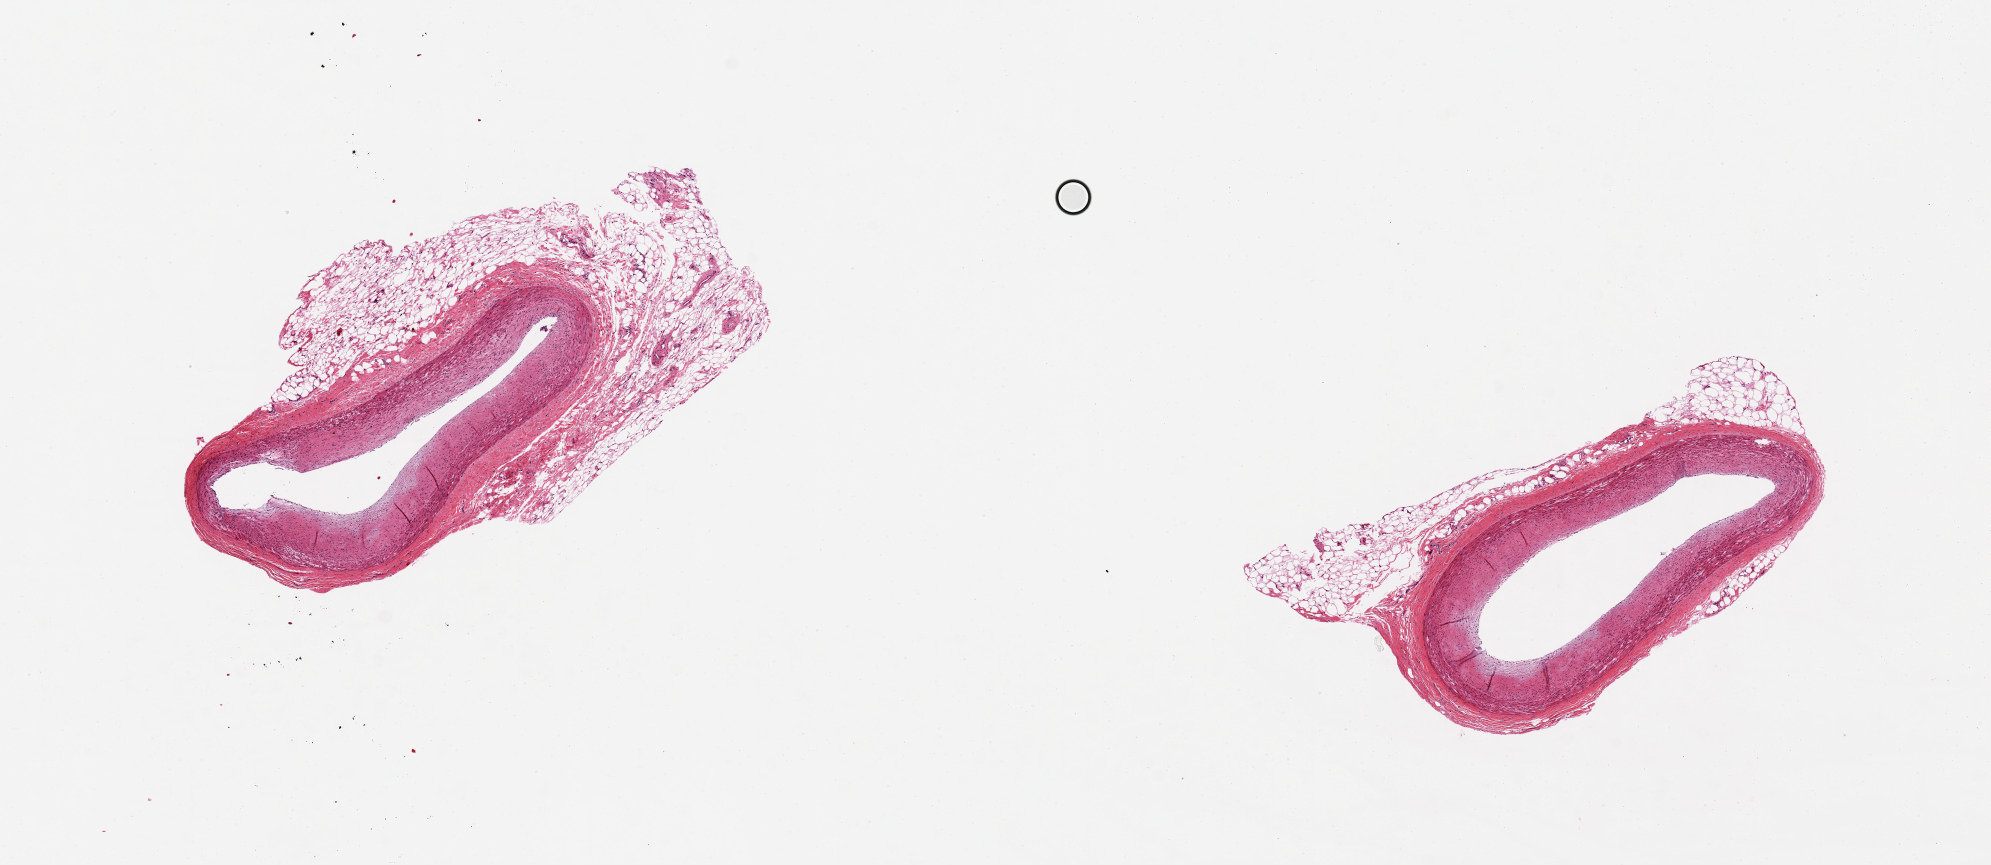
Hematoxylin and eosin (H&E) whole-slide image — shown as a low-resolution overview of the whole scanned area (about 15.8 x 6.8 mm, acquisition: 20x scan); PAXgene-fixed, paraffin-embedded tissue; target tissue: coronary artery; tissue donor sample.
Pathologist's review note for this sample: Incorrect tissue. 2 pieces of coronary artery autolysis score 0-1. one piece about 50% fat.